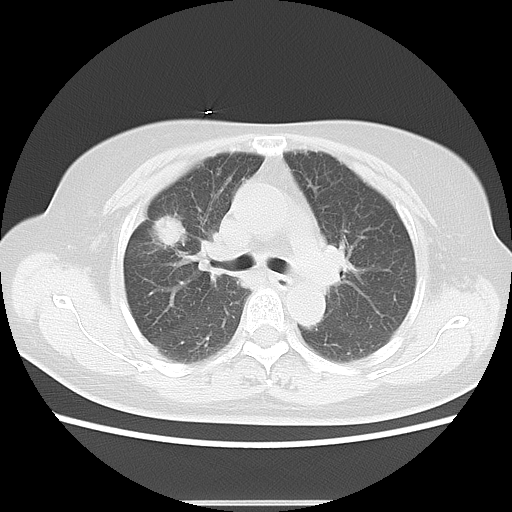
Chest CT, one axial slice. Position 8 of 15 along the scan axis. Lung window (W 1500 / L -600 HU). 512 × 512 image matrix, field of view 350 × 350 mm. Patient: female, 57 years. From the clinical record (not read from this slice): clinical TNM (as recorded): T1c N1 M0.
Outlined on this slice (bounding box drawn by a radiologist):
- lung tumour (recorded histology: adenocarcinoma): bounding box <154,210,188,253> (left, top, right, bottom; pixels)